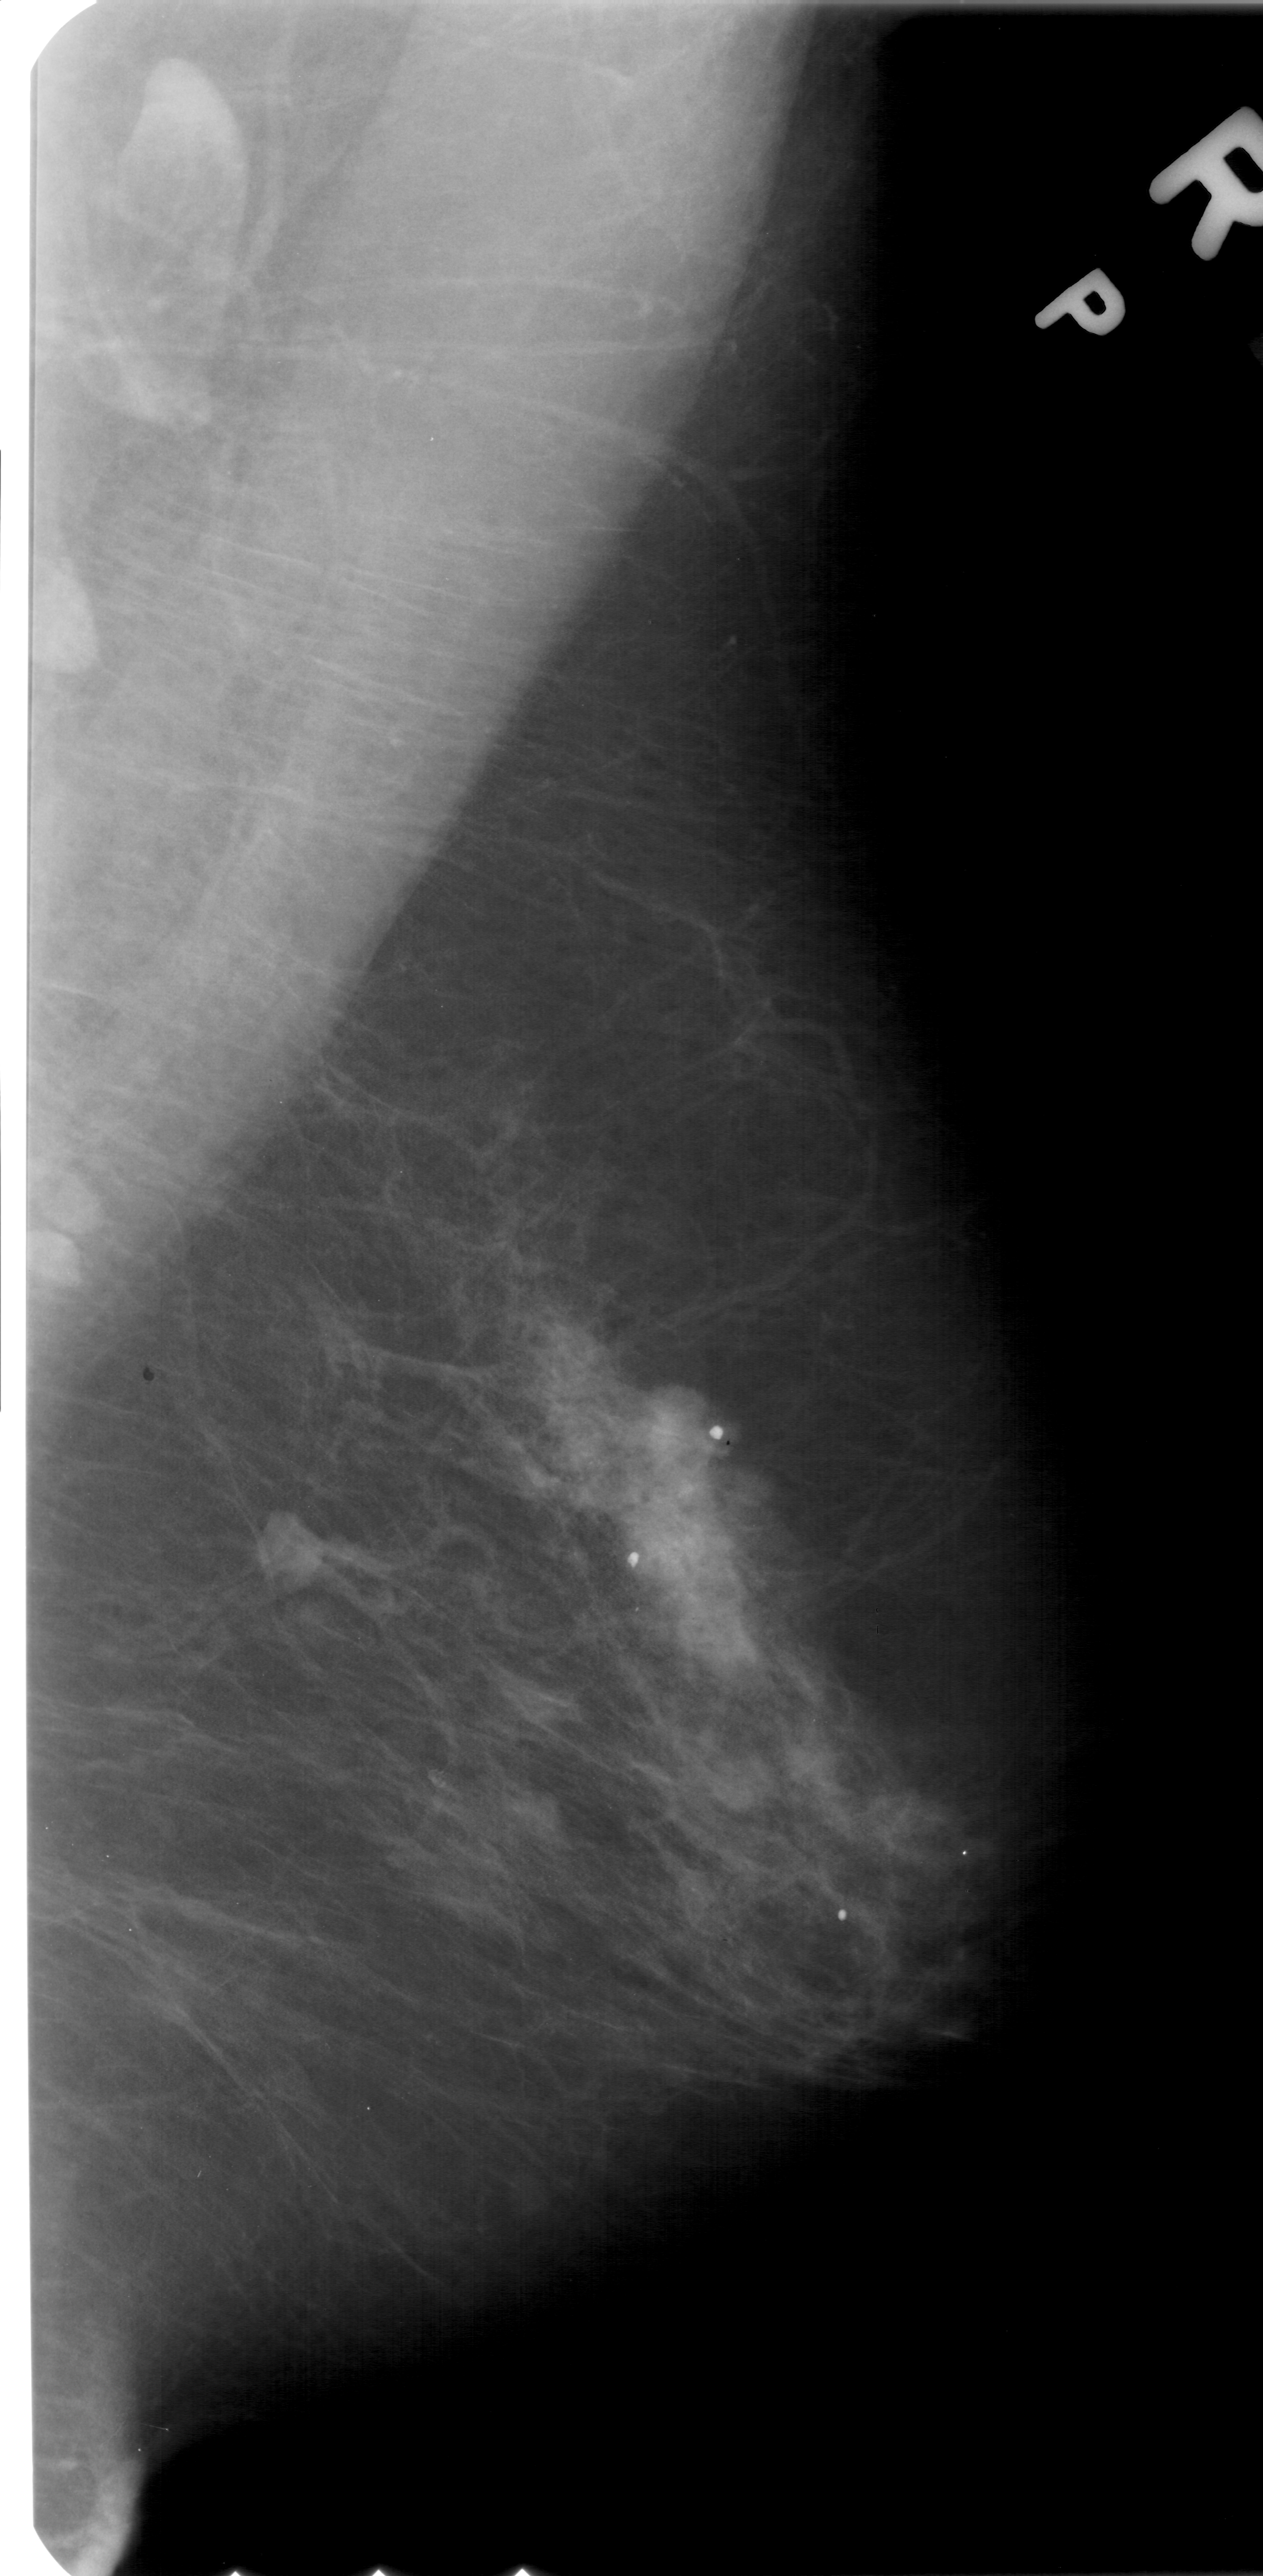
Scanned film-screen mammogram; right breast; MLO view; breast composition: heterogeneously dense (BI-RADS density category 3 of 4).
Mass, shape lobulated, margins circumscribed; BI-RADS assessment category 4; pathology (as recorded): benign.